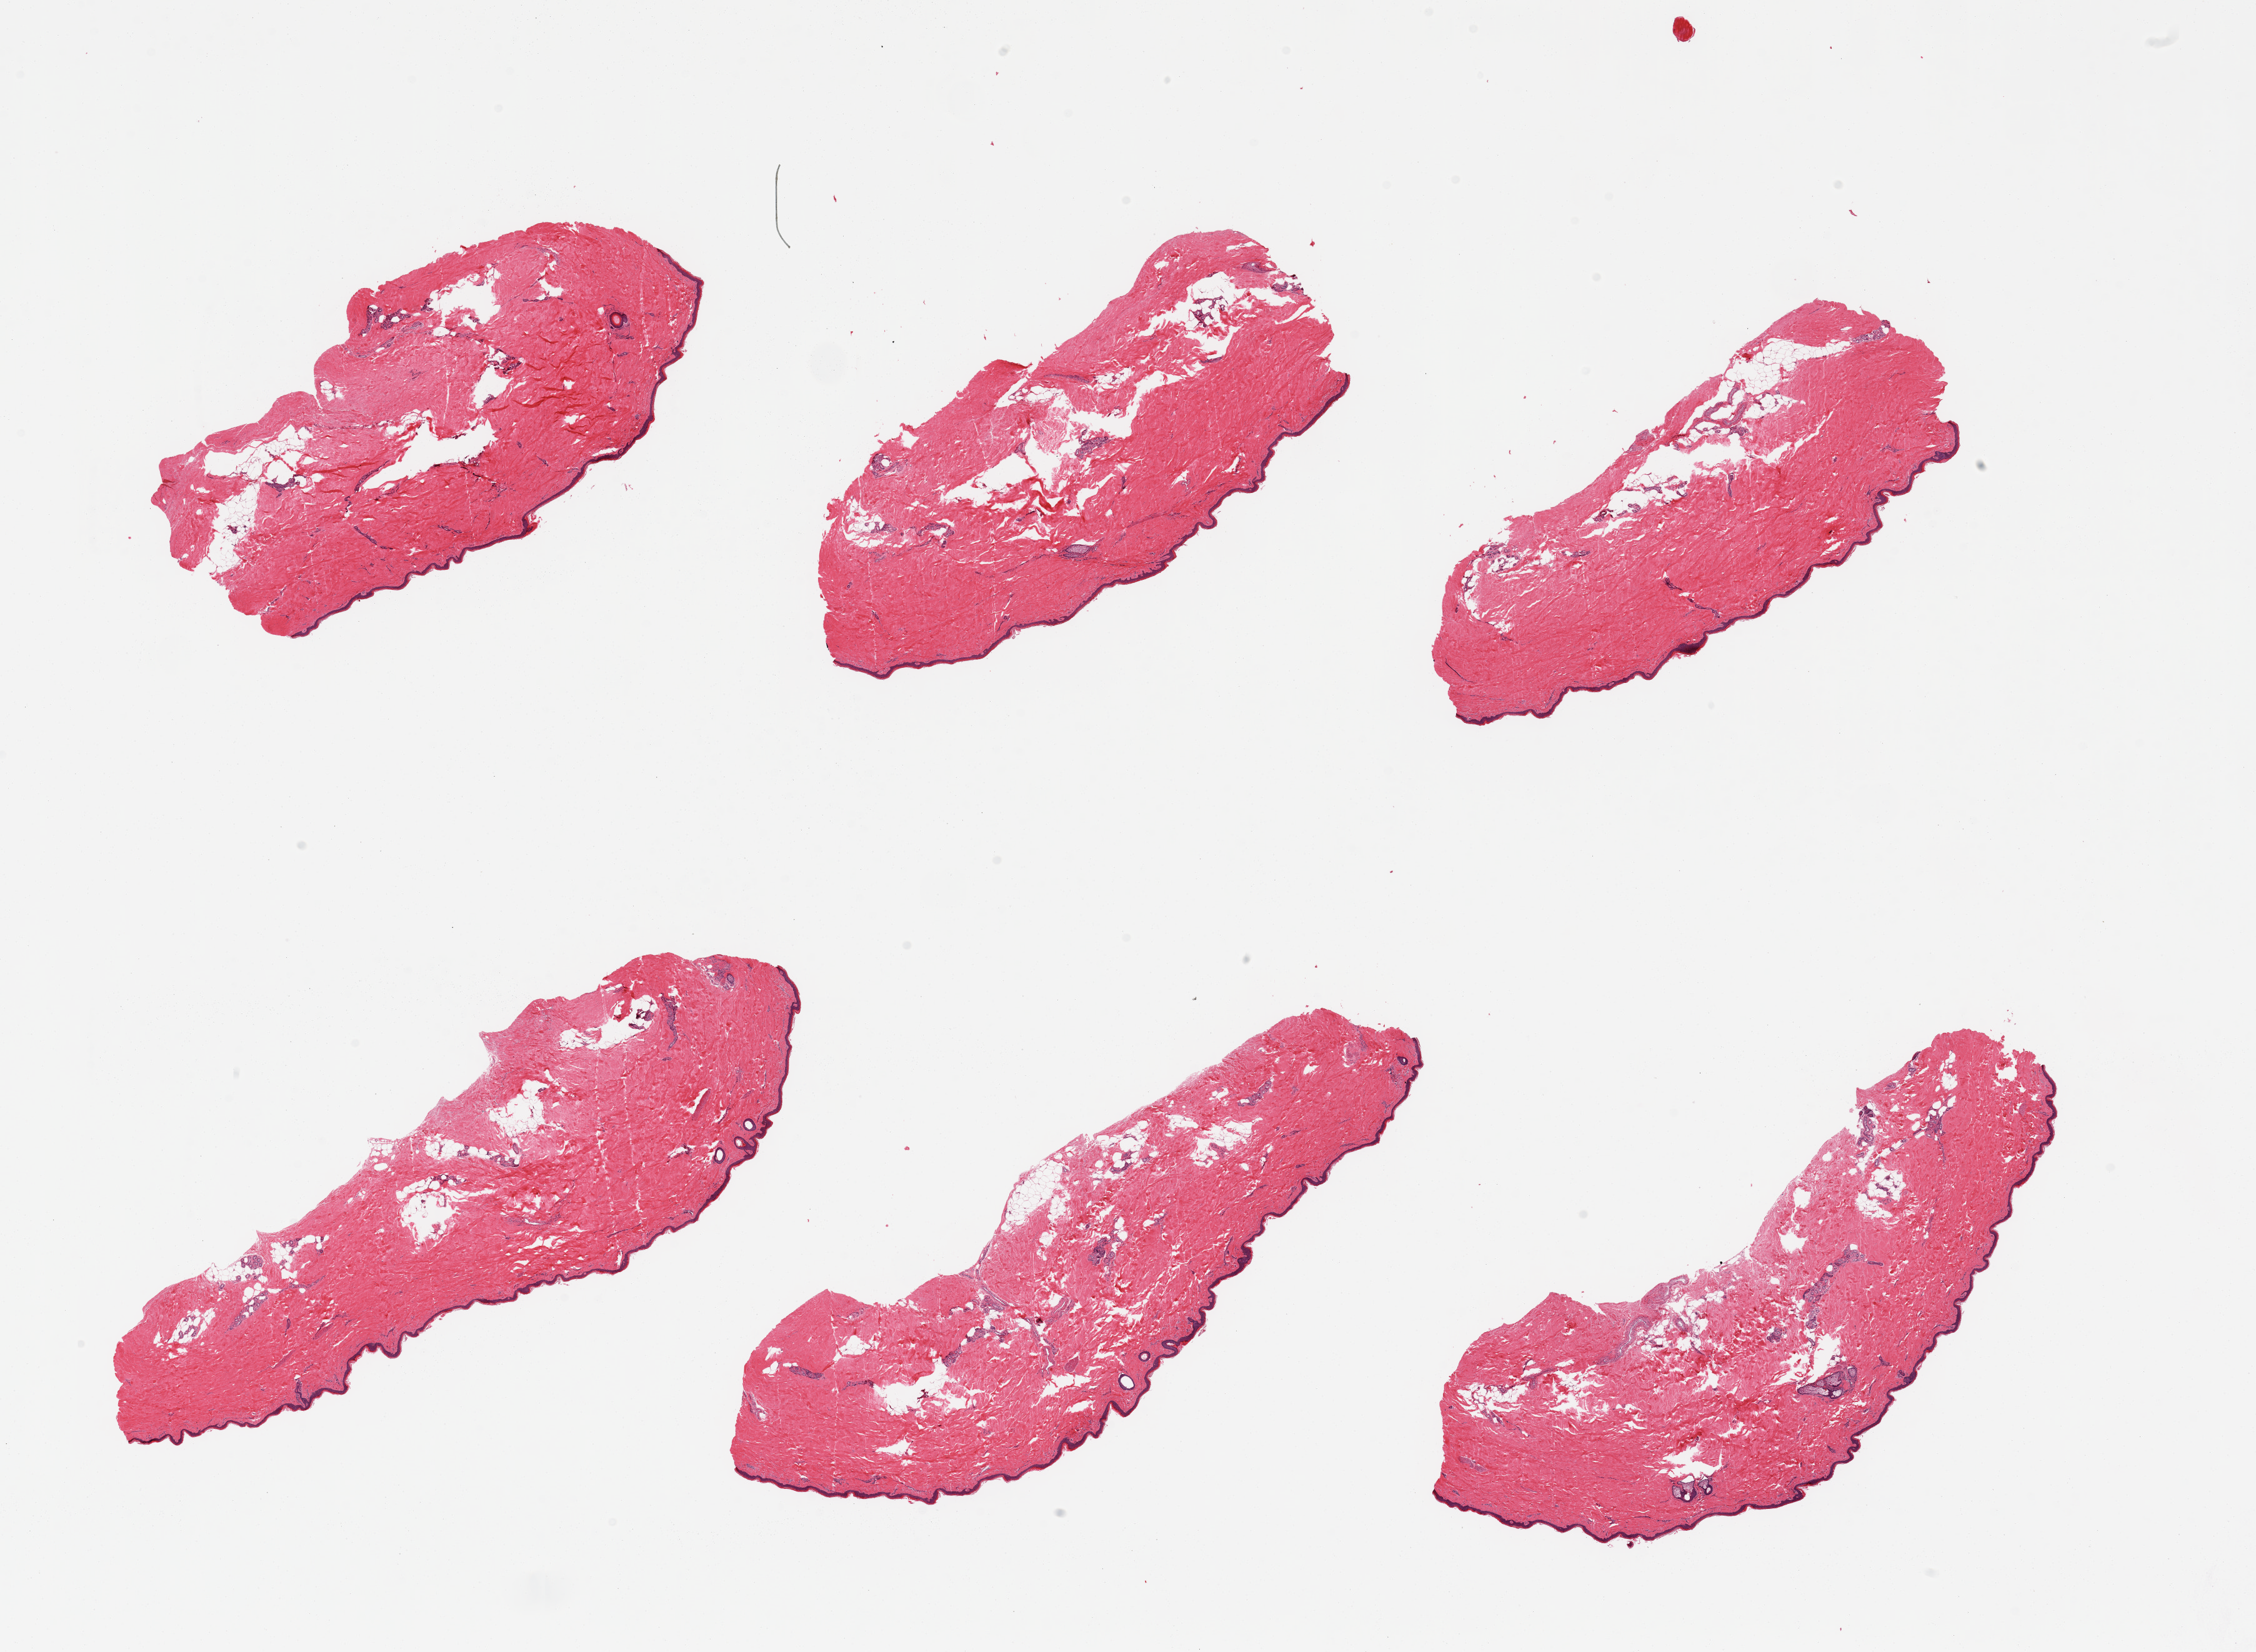
H&E whole-slide image, shown as a low-resolution overview of the whole scanned area (about 28.5 x 20.9 mm). PAXgene-fixed, paraffin-embedded tissue. Sampled site (target tissue): skin of lower leg. Tissue donor sample. Donor sex: male.
Review note (as recorded): 6 pieces; 10% intradermal fat; well trimmed.